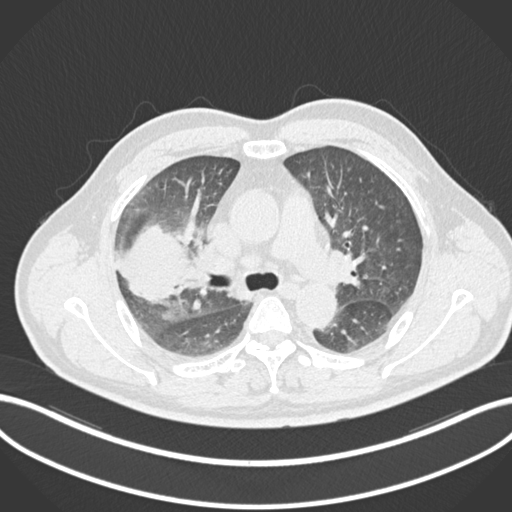
Chest CT, one axial slice. Position 650 of 852 along the scan axis. Lung window (W 1500 / L -600 HU). 512 × 512 image matrix, field of view 400 × 400 mm. Patient: male, 55 years. From the clinical record (not read from this slice): clinical TNM (as recorded): T3 N2 M1.
Outlined on this slice (rectangle marked by the reading radiologist):
- lung tumour (recorded histology: adenocarcinoma): bounding box (x1, y1, x2, y2) in pixels: (117, 224, 196, 303)